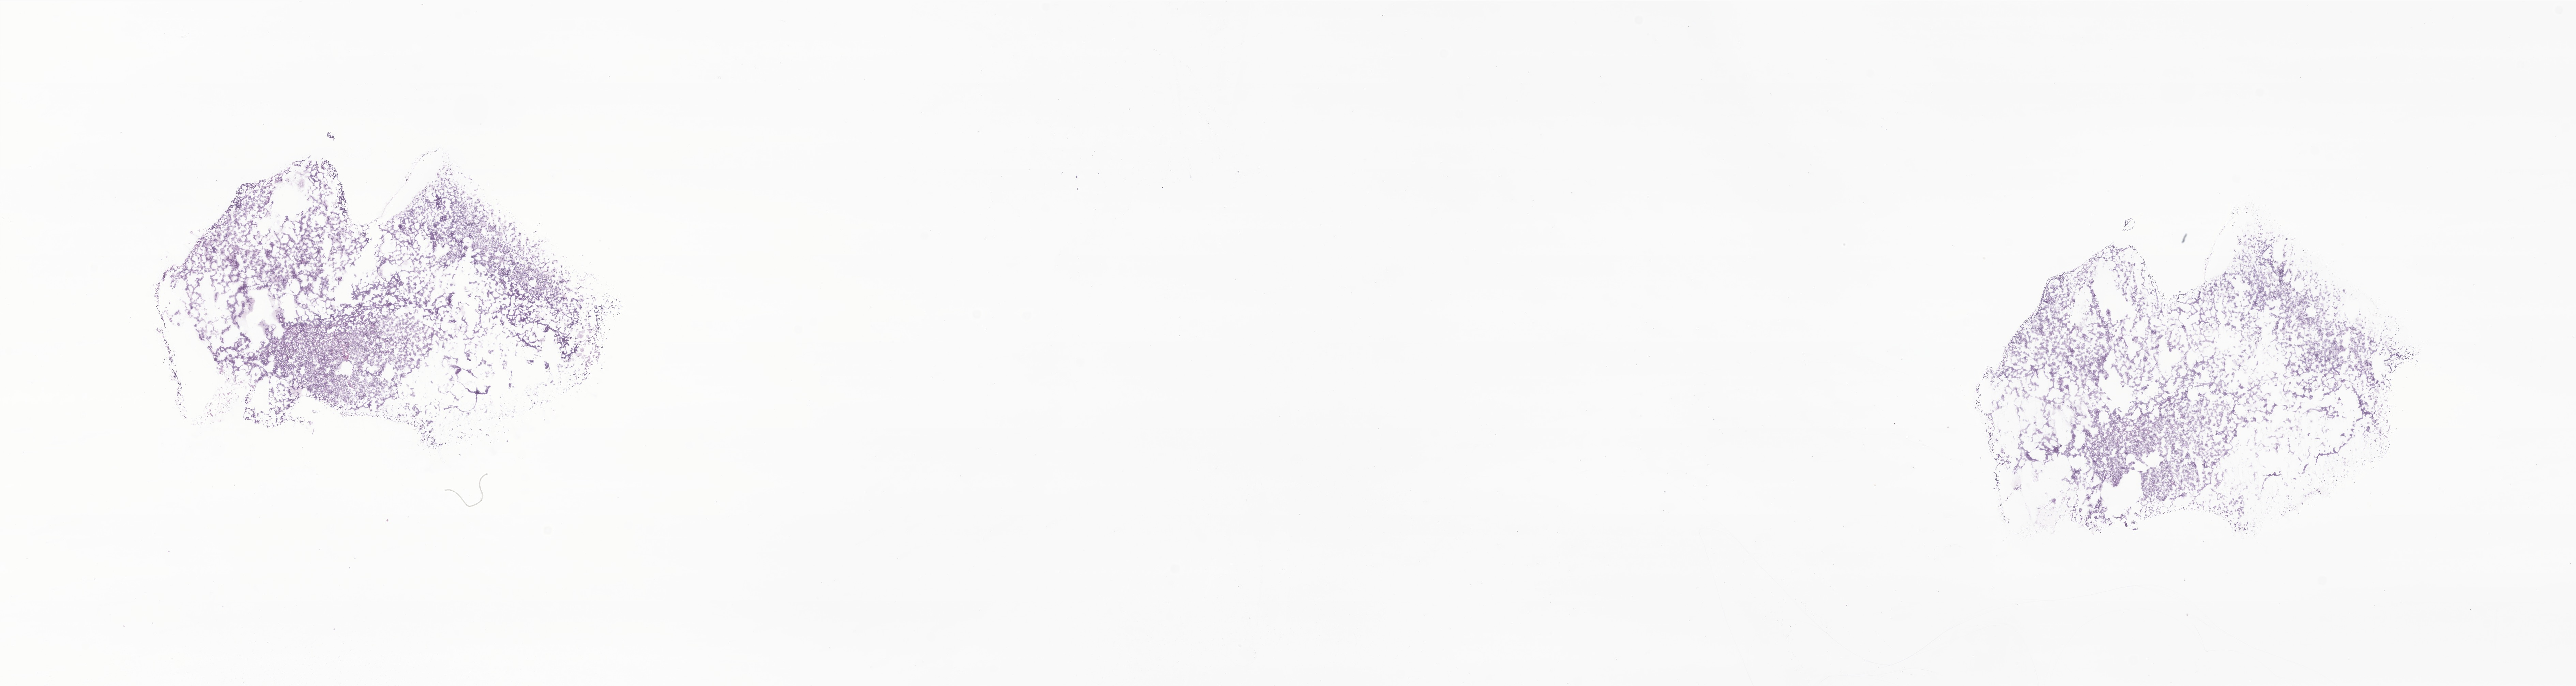
Digitized haematoxylin and eosin-stained section of tumor tissue from the cerebellum, whole scanned area (about 31.9 x 8.5 mm) shown as a low-resolution overview, cryosection (OCT / tissue freezing medium). Patient: male, age 123 months (10 years 3 months).
* recorded diagnosis: Medulloblastoma, NOS